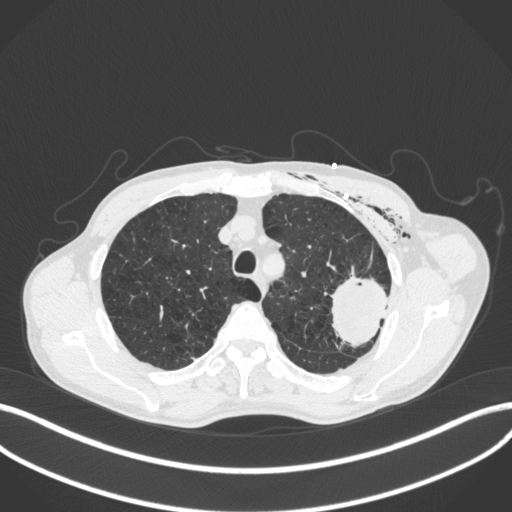
Chest CT, one axial slice; reconstruction kernel B31f; 120 kVp; lung window (W 1500 / L -600 HU); 1 mm slice thickness; 512 × 512 image matrix. Patient: male, 58 years. Case-level facts recorded for this patient, not image findings: clinical TNM (as recorded): T3 N0 M0.
Outlined on this slice (rectangle marked by the reading radiologist):
- lung tumour (recorded histology: adenocarcinoma): box from (x=326, y=269) to (x=399, y=352) px